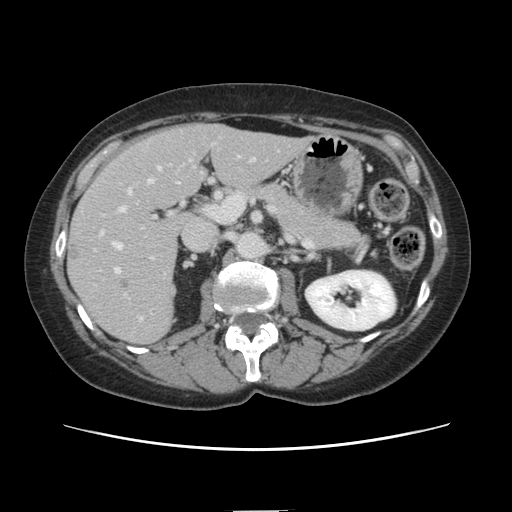
Contrast-enhanced abdominal CT, one axial slice; position 69 of 141 along the scan axis; intravenous contrast given; soft-tissue window (W 400 / L 40 HU); 512 × 512 image matrix, field of view 350 × 350 mm. Female patient, age 63 years. From the clinical record (not read from this slice): diagnosis: colorectal cancer liver metastases, imaged before liver resection; multiple liver metastases: yes; largest metastasis: 3.2 cm.
Outlined on this slice (outlined manually by an expert reader):
- hepatic veins: bounding box [x1, y1, x2, y2] px = [114, 167, 160, 274]
- liver: [69, 125, 307, 344]
- planned liver remnant (the part of the liver to remain after resection): [175, 125, 308, 191]
- portal vein (with intrahepatic branches): [101, 159, 253, 319]
- liver metastasis: [118, 279, 129, 289]
- liver metastasis: [67, 243, 81, 261]